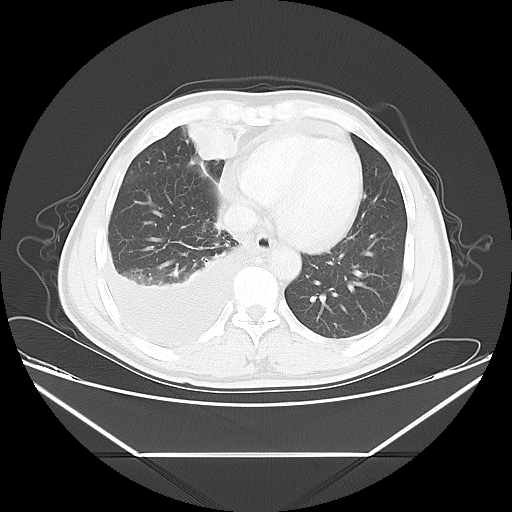
Chest CT, one axial slice; position 16 of 56 along the scan axis; lung window (W 1500 / L -600 HU); 5 mm slice thickness; 512 × 512 image matrix, field of view 412 × 412 mm. Patient: male, 57 years. From the clinical record (not read from this slice): clinical TNM (as recorded): T2 N3 M1.
Outlined on this slice (rectangle marked by the reading radiologist):
- lung tumour (recorded histology: adenocarcinoma): box from (x=181, y=117) to (x=245, y=165) px